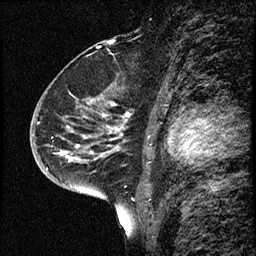
Breast MRI (dynamic contrast-enhanced), one sagittal slice. Position 41 of 68 along the scan axis. Dynamic contrast-enhanced study with each time point stored as its own series, time point 2 of 3 at this slice position (early post-contrast, ordered by acquisition time). 1.5 T. TE 4.2 ms, TR 17.6 ms. 2 mm slice thickness. 256 × 256 image matrix. Patient: female, 52 years. From the clinical record (not read from this slice): setting: breast cancer imaged before/during neoadjuvant chemotherapy; receptor status: HER2-positive.
Outlined on this slice (semi-automatically segmented with operator editing):
- analysis volume of interest (the breast-tissue region the enhancement analysis was run in; not a lesion): box from (x=50, y=61) to (x=141, y=184) px
- tumour enhancement mask (voxels above the 100 % enhancement threshold inside the analysis volume of interest): (x=61, y=104)–(x=122, y=160)